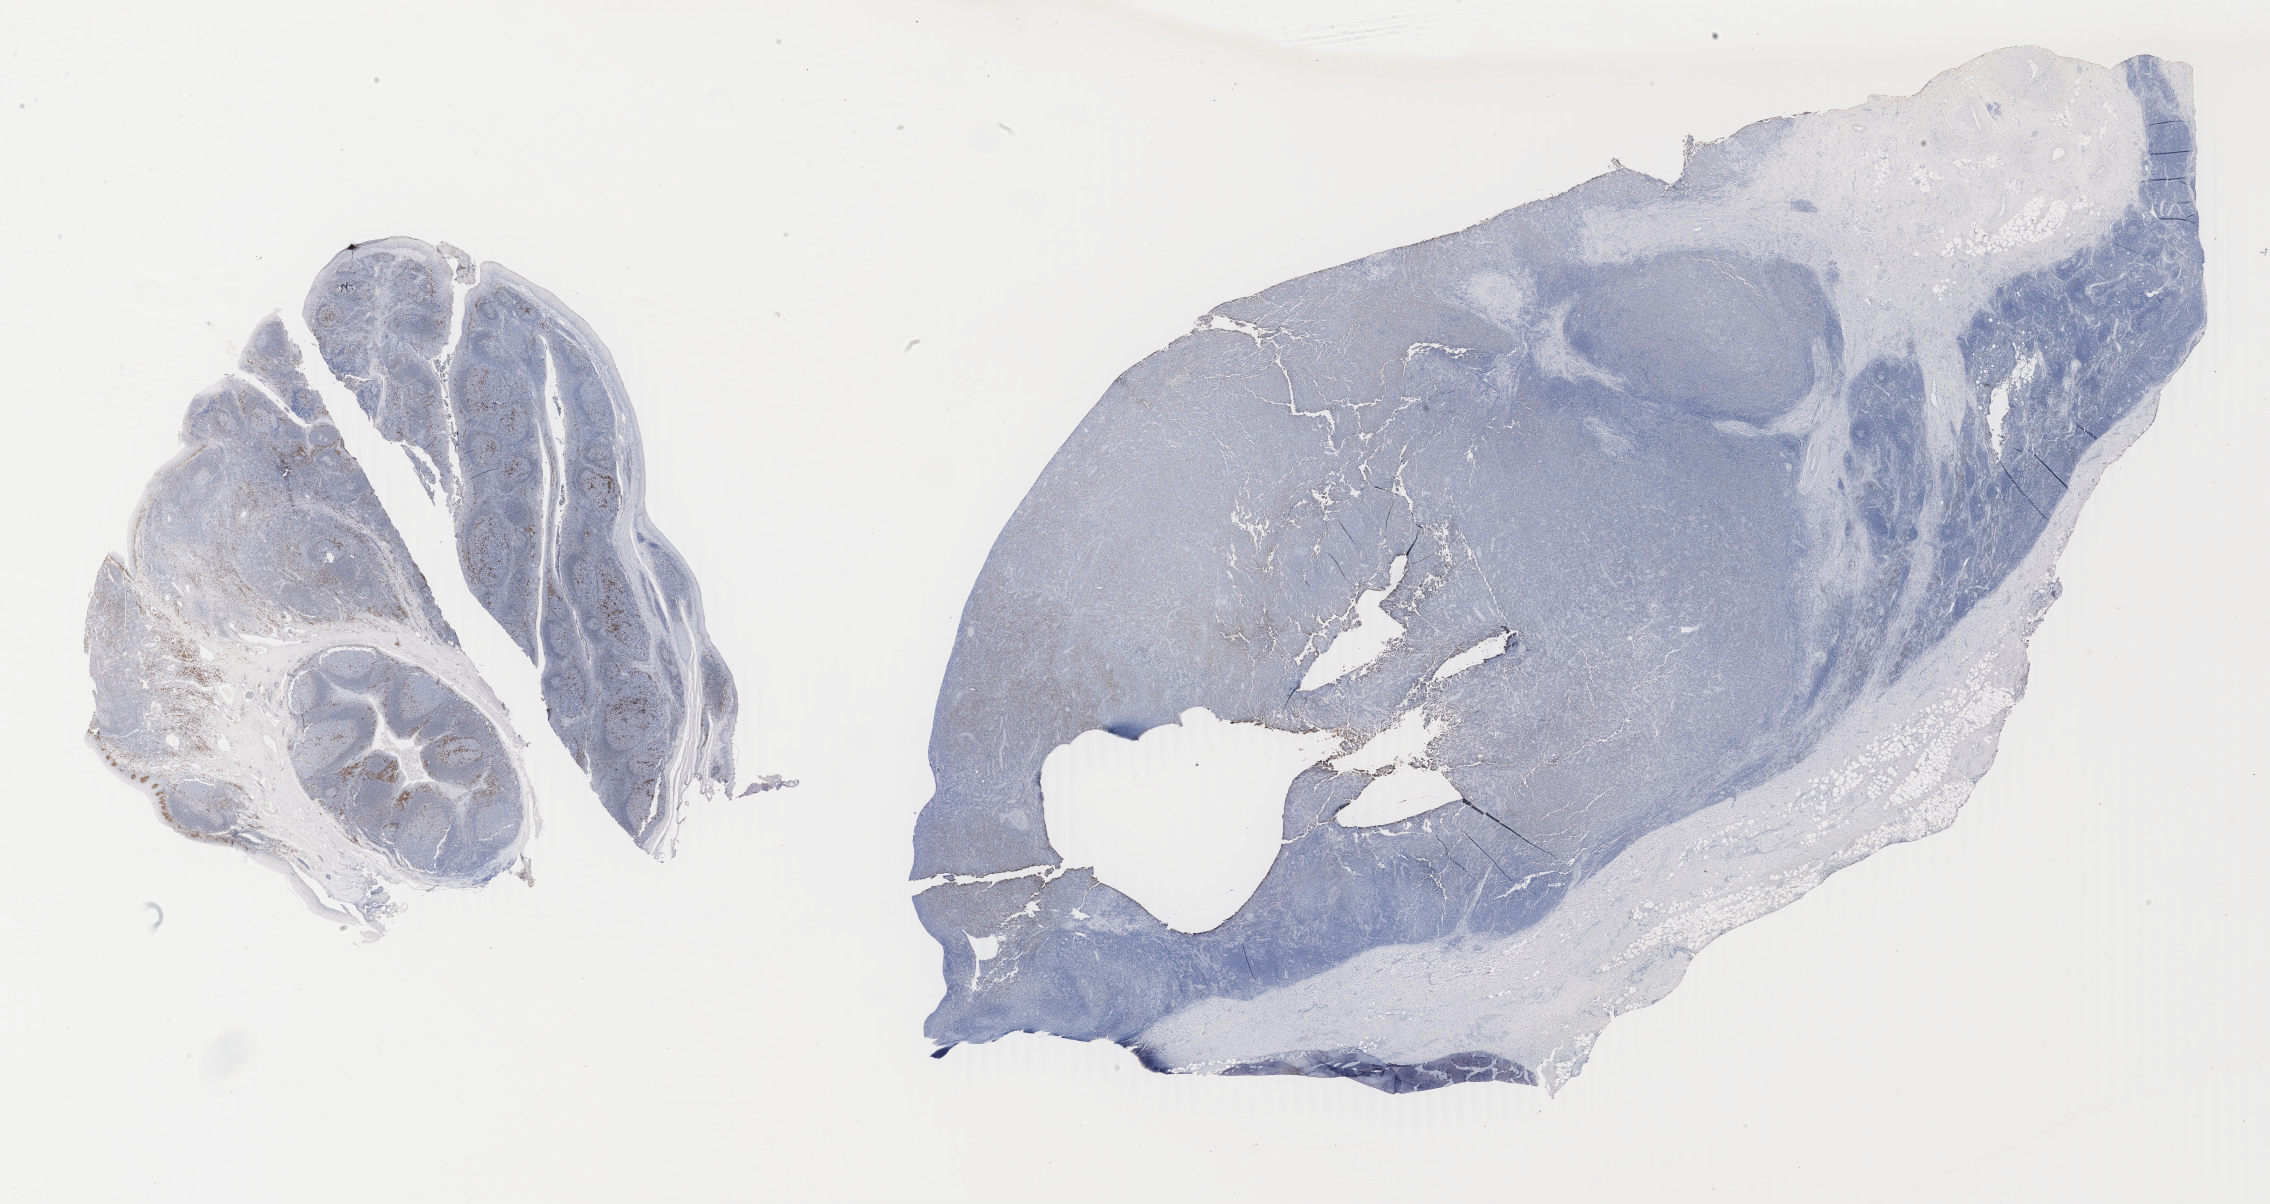
Whole-slide image, immunohistochemical stain for IRF4/MUM1, a low-resolution overview of the entire scanned area, about 36.1 x 19.1 mm, specimen: tumor tissue, anatomic site: lymph node. Patient: male, 60 years old.
Histologic diagnosis: Diffuse large B-cell lymphoma, NOS.